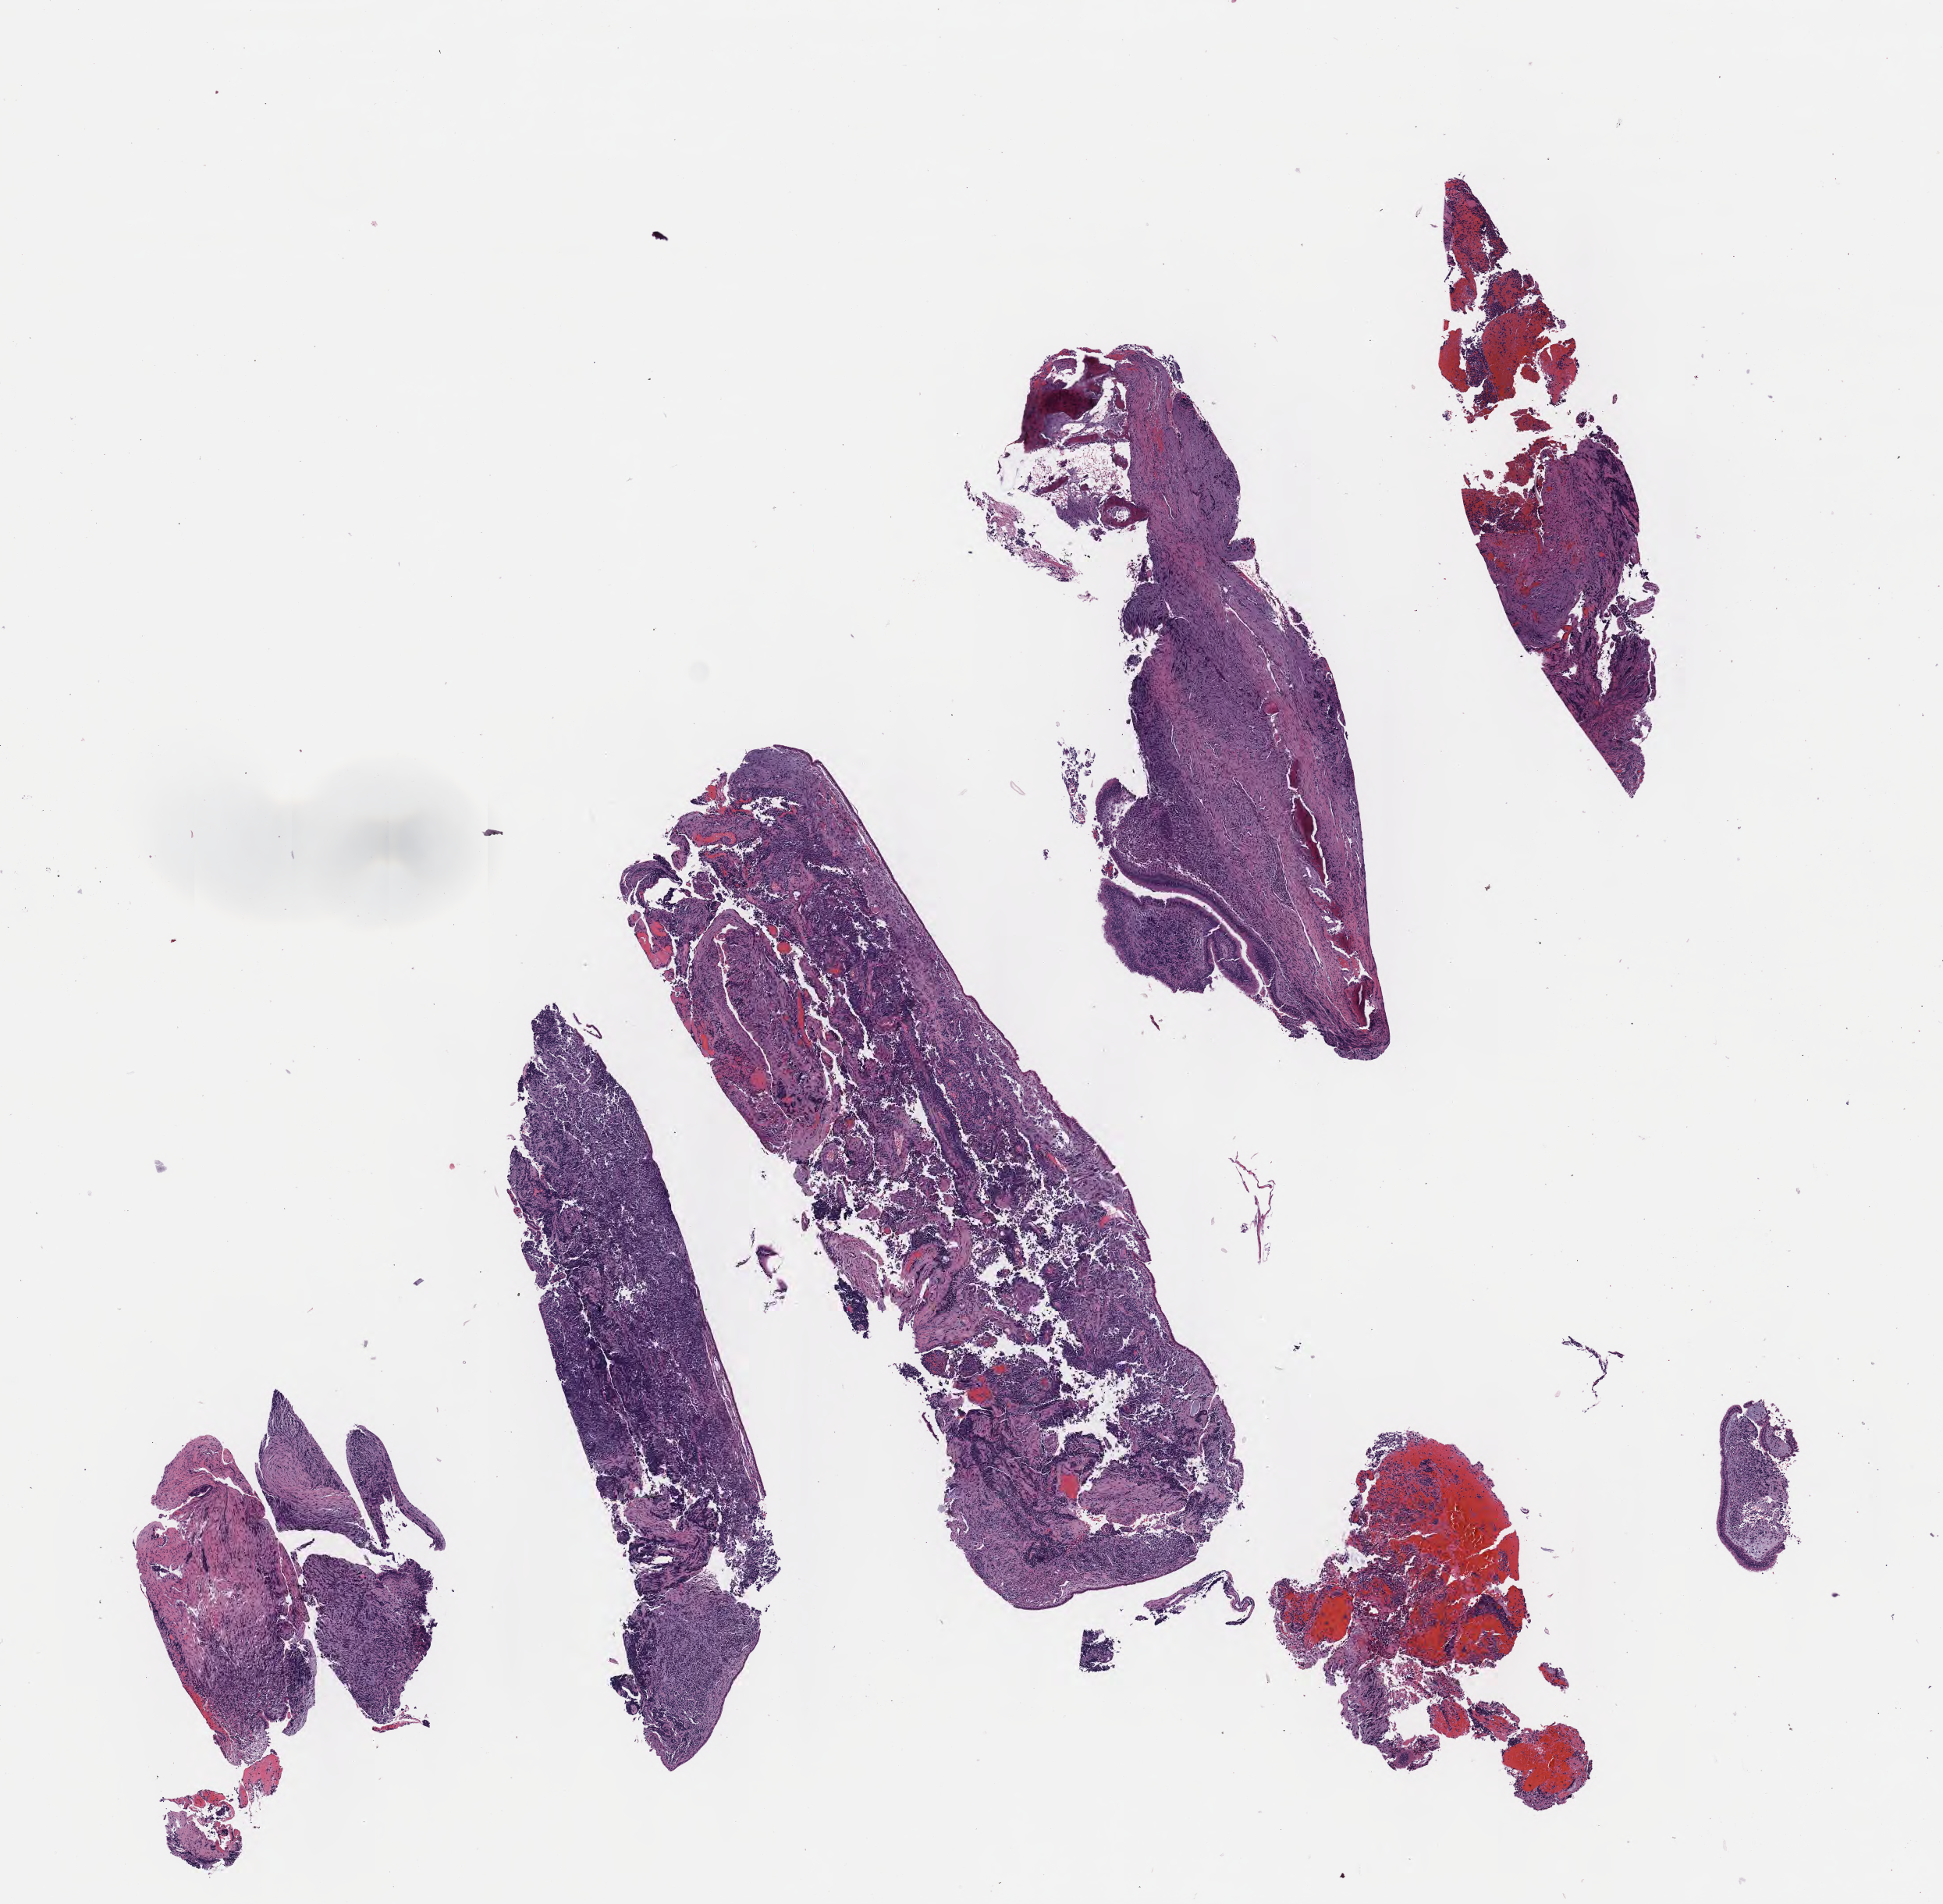
Whole-slide image, haematoxylin and eosin stain of tumor tissue from the ethmoid sinus — whole scanned area (about 10.1 x 9.9 mm) shown as a low-resolution overview, formalin-fixed paraffin-embedded section. Patient male; age 131 months (10 years 11 months).
• recorded diagnosis: Alveolar rhabdomyosarcoma